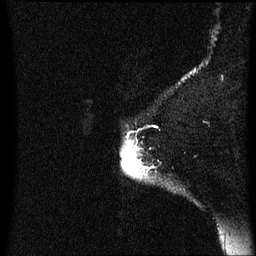
Breast MRI (dynamic contrast-enhanced), one sagittal slice; slice 56 of 60 in the series (ordered by position); dynamic contrast-enhanced series, image 2 of 3 at this slice position (ordered by acquisition); 1.5 T; TE 4.2 ms, TR 8.4 ms; 2 mm slice thickness; 256 × 256 image matrix. Female patient, age 54 years. From the clinical record (not read from this slice): setting: breast cancer imaged before/during neoadjuvant chemotherapy; receptor status: HR-positive, HER2-negative.
Structures marked on this image (semi-automatic segmentation, software-assisted and operator-edited):
- analysis volume of interest (the breast-tissue region the enhancement analysis was run in; not a lesion): bounding box <123,140,149,179> (left, top, right, bottom; pixels)
- tumour enhancement mask (voxels above the 70 % enhancement threshold inside the analysis volume of interest): <123,140,145,177>